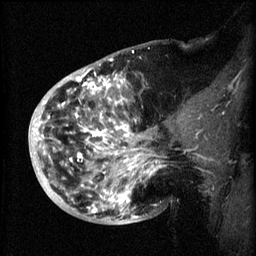
Breast MRI (dynamic contrast-enhanced), one sagittal slice. Position 21 of 60 along the scan axis. 3 images stored at this slice position (order not interpretable as contrast timing). 1.5 T. TE 4.2 ms, TR 8.2 ms. 2 mm slice thickness. 256 × 256 image matrix, field of view 200 × 200 mm. Female patient, age 50 years.
Structures marked on this image (semi-automatically segmented with operator editing):
- analysis volume of interest (the breast-tissue region the enhancement analysis was run in; not a lesion): bounding box (x1, y1, x2, y2) in pixels: (44, 72, 173, 219)
- tumour enhancement mask (voxels above the 70 % enhancement threshold inside the analysis volume of interest): (44, 74, 162, 219)